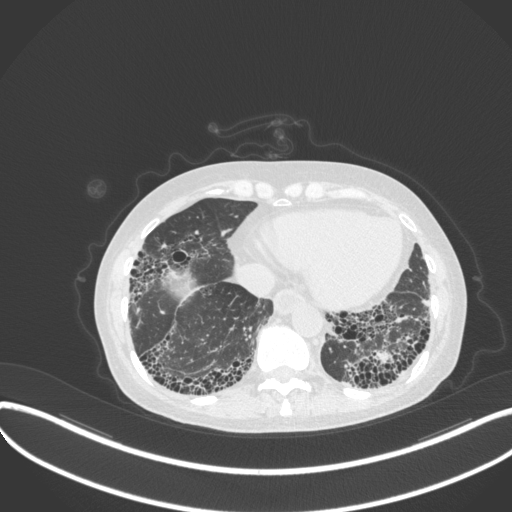
Chest CT, one axial slice; position 77 of 373 along the scan axis; lung window (W 1500 / L -600 HU); 1 mm slice thickness; 512 × 512 image matrix, field of view 400 × 400 mm. Patient: female, 56 years. From the clinical record (not read from this slice): clinical TNM (as recorded): T1 N0 M0.
Outlined on this slice (bounding box drawn by a radiologist):
- lung tumour (recorded histology: adenocarcinoma): bounding box (x1, y1, x2, y2) in pixels: (369, 347, 396, 368)